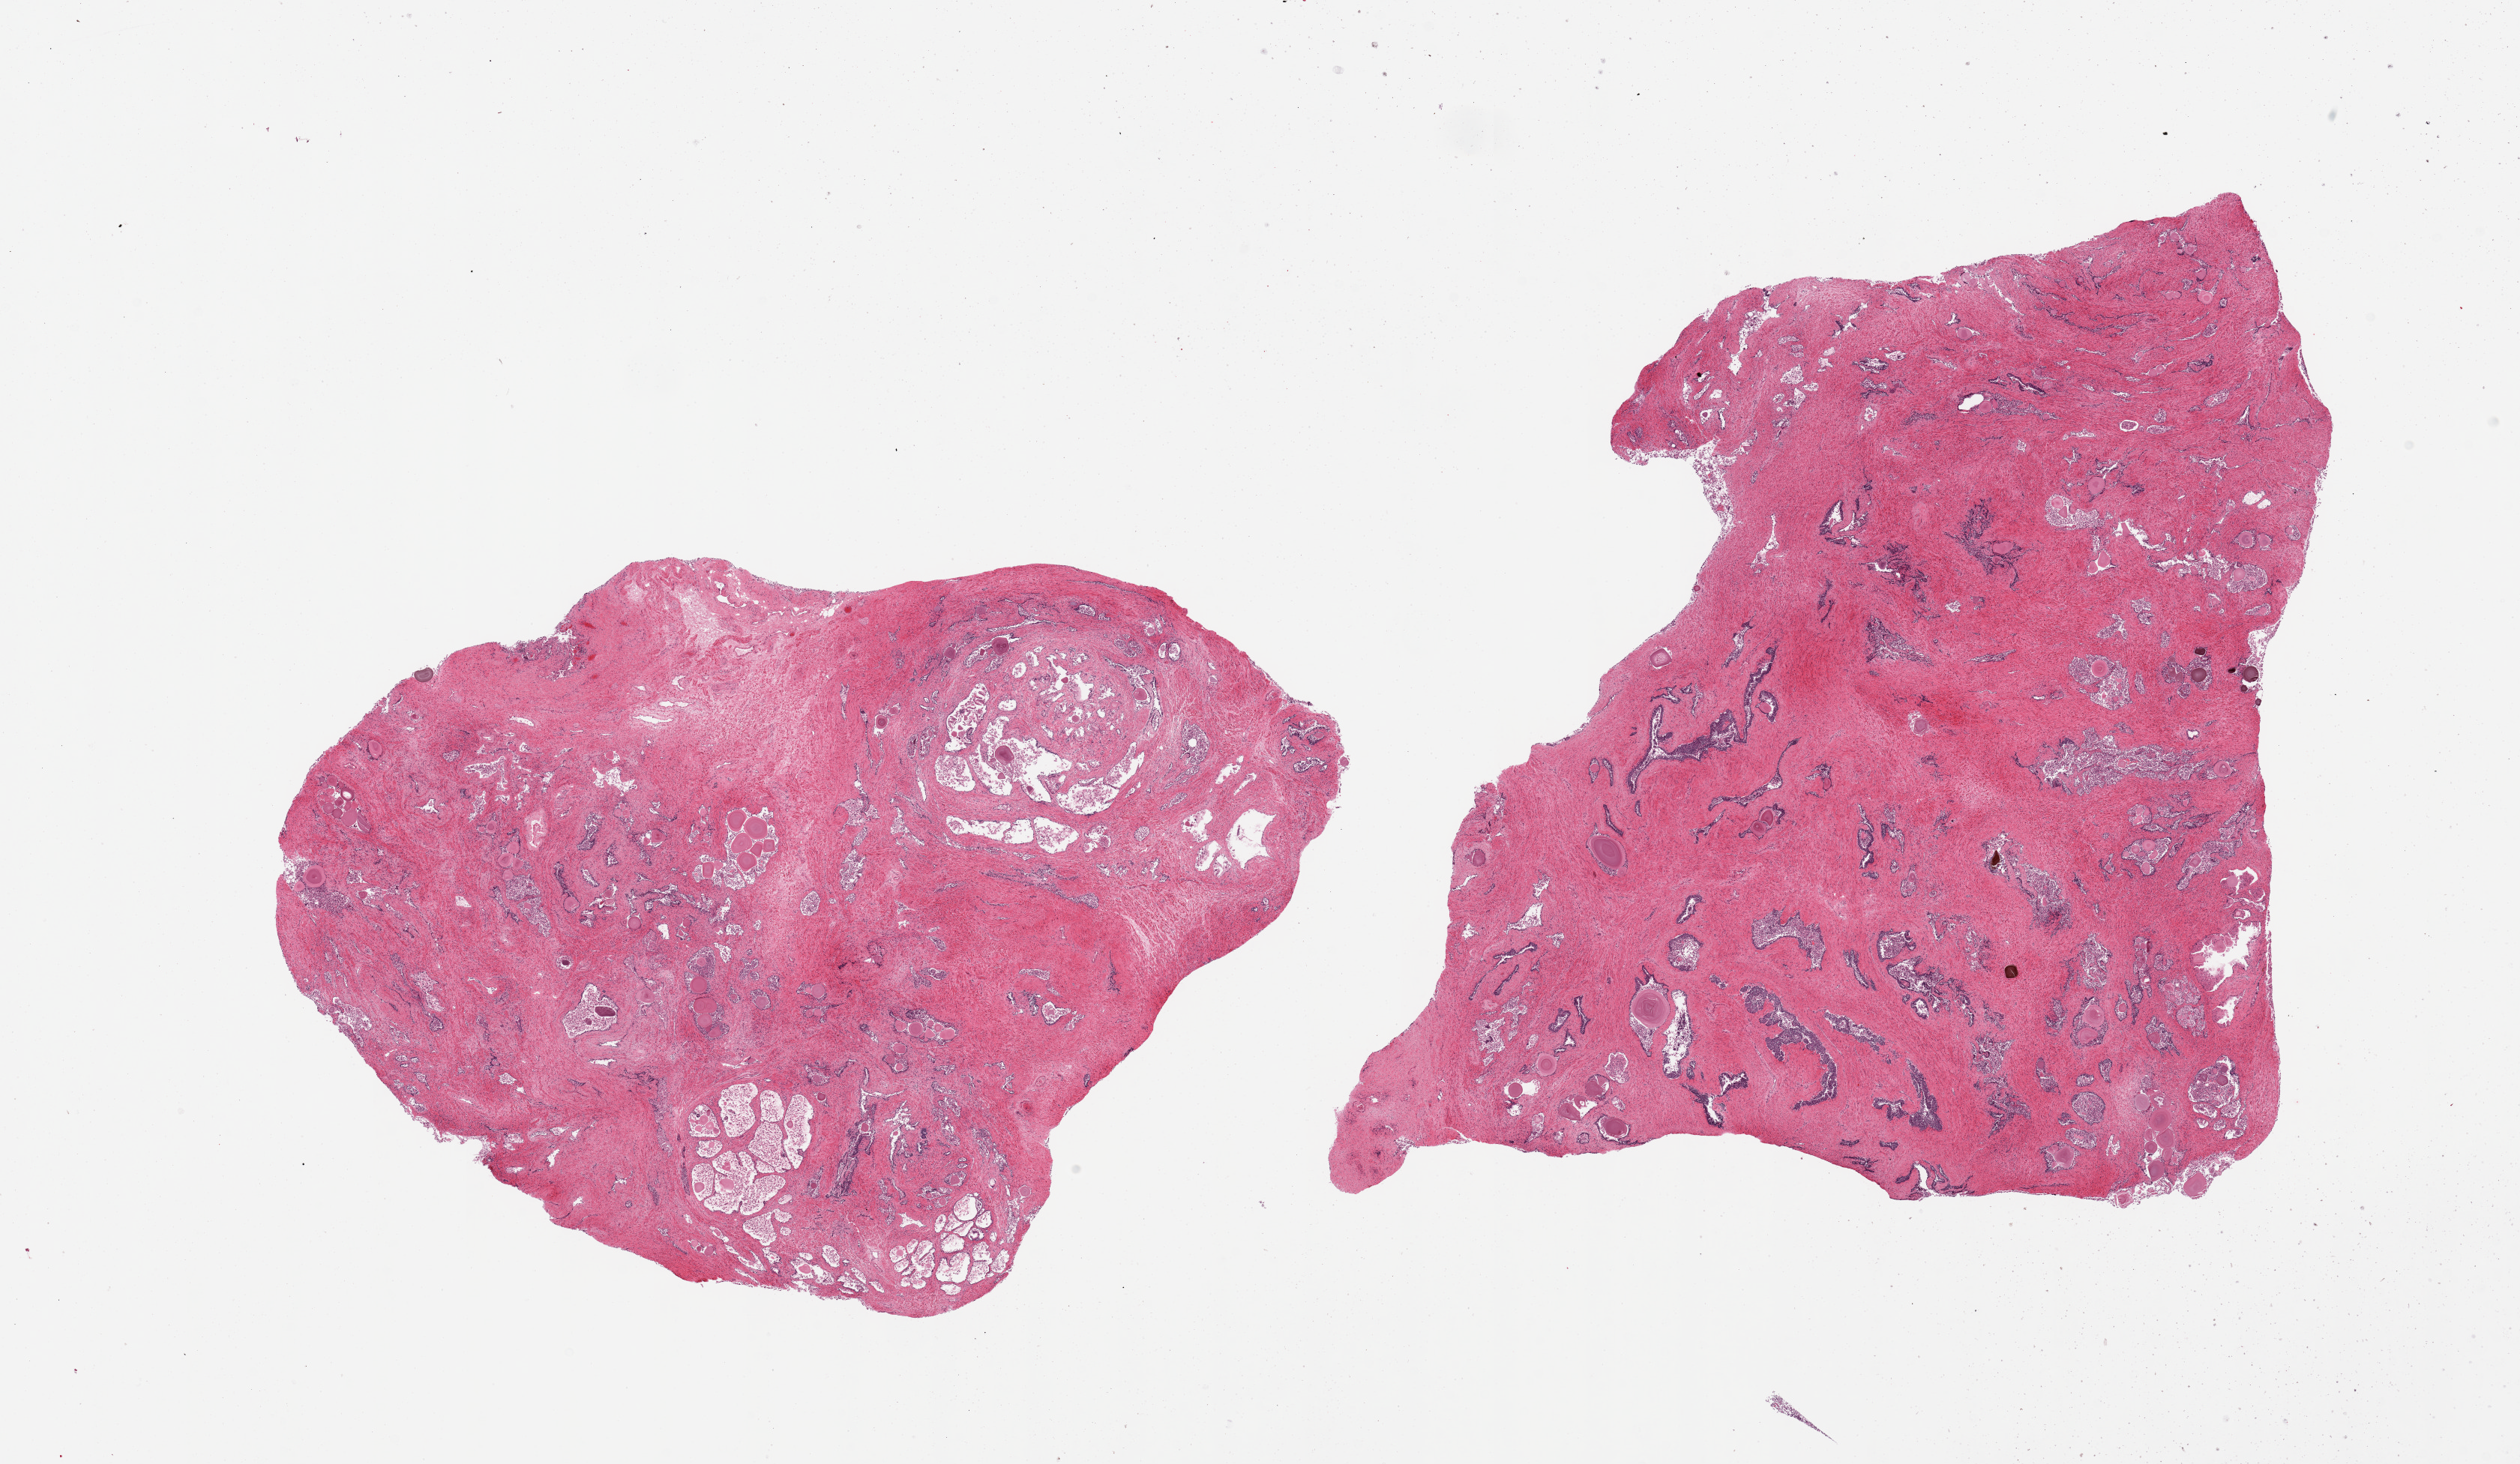
H&E whole-slide image, low-resolution overview of the scanned area, about 26.6 x 15.4 mm; PAXgene-fixed paraffin-embedded (PFPE) section; section of prostate (target tissue); tissue donor sample. Male donor.
• reviewer comment on this tissue sample: 2 pieces. Glands completely autolyzed; stroma preserved